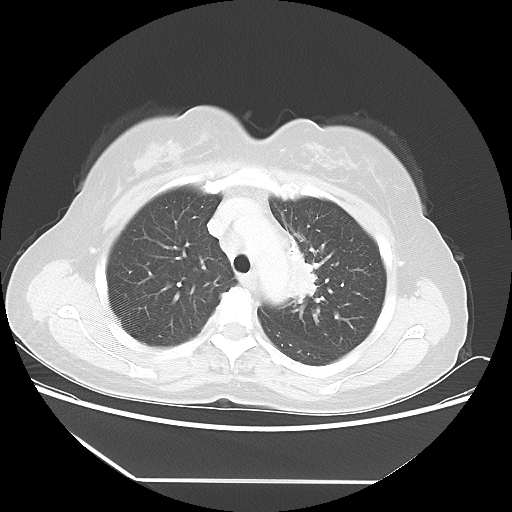
Chest CT, one axial slice. Position 39 of 52 along the scan axis. 100 kVp. Lung window (W 1500 / L -600 HU). 5 mm slice thickness. 512 × 512 image matrix, field of view 390 × 390 mm. Patient: female, 50 years. Case-level facts recorded for this patient, not image findings: clinical TNM (as recorded): T2 N3 M0.
Structures marked on this image (bounding box drawn by a radiologist):
- lung tumour (recorded histology: adenocarcinoma): bounding box [x1, y1, x2, y2] px = [275, 250, 328, 316]